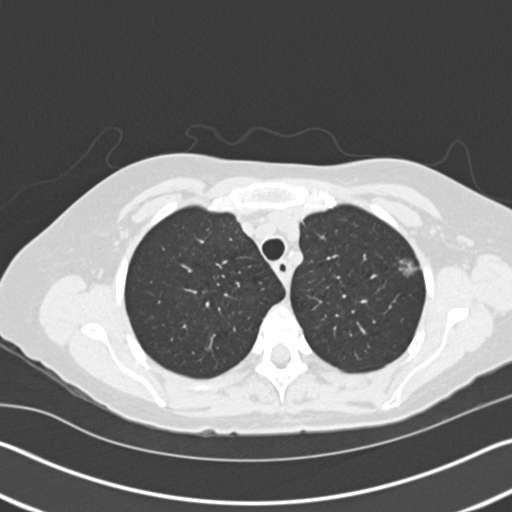
Low-dose screening chest CT, axial slice. Baseline annual screen. Lung window (W 1500 / L -600 HU). 2 mm slice thickness. Standard (soft-tissue) reconstruction kernel (B30f). Female, age 60 years at enrolment.
- Expert reader's lesion annotation, bounding box [x1, y1, x2, y2] px = [386, 247, 439, 289].
- The screening reader recorded 2 non-calcified nodules or masses ≥4 mm on this exam; which of them this box marks is not recorded.
- Official screen result: positive, change unspecified: nodule(s) >= 4 mm or enlarging nodule(s), mass(es), or other non-specific abnormalities suspicious for lung cancer.
- Participant outcome: lung cancer diagnosed 417 days after this screen — adenocarcinoma, NOS, left upper lobe, moderately differentiated (G2), stage IA (AJCC 6th edition), 11 mm at pathology.